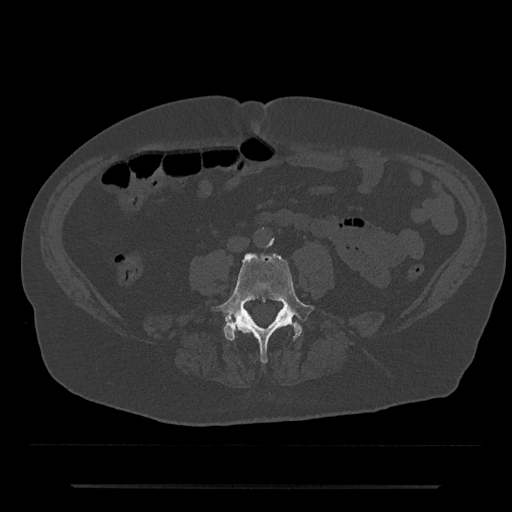
CT including the spine, one axial slice; reconstruction kernel Br40s/3; bone window (W 1800 / L 400 HU); 0.5 mm slice thickness; 512 × 512 image matrix, field of view 434 × 434 mm. Male patient, age 80 years. From the clinical record (not read from this slice): primary cancer: prostate; vertebrae with lytic lesions (as recorded): L1, T11.
Annotated regions visible in this slice (semi-automatic segmentation, software-assisted and operator-edited):
- L4 vertebra: bounding box <215,253,315,363> (left, top, right, bottom; pixels)